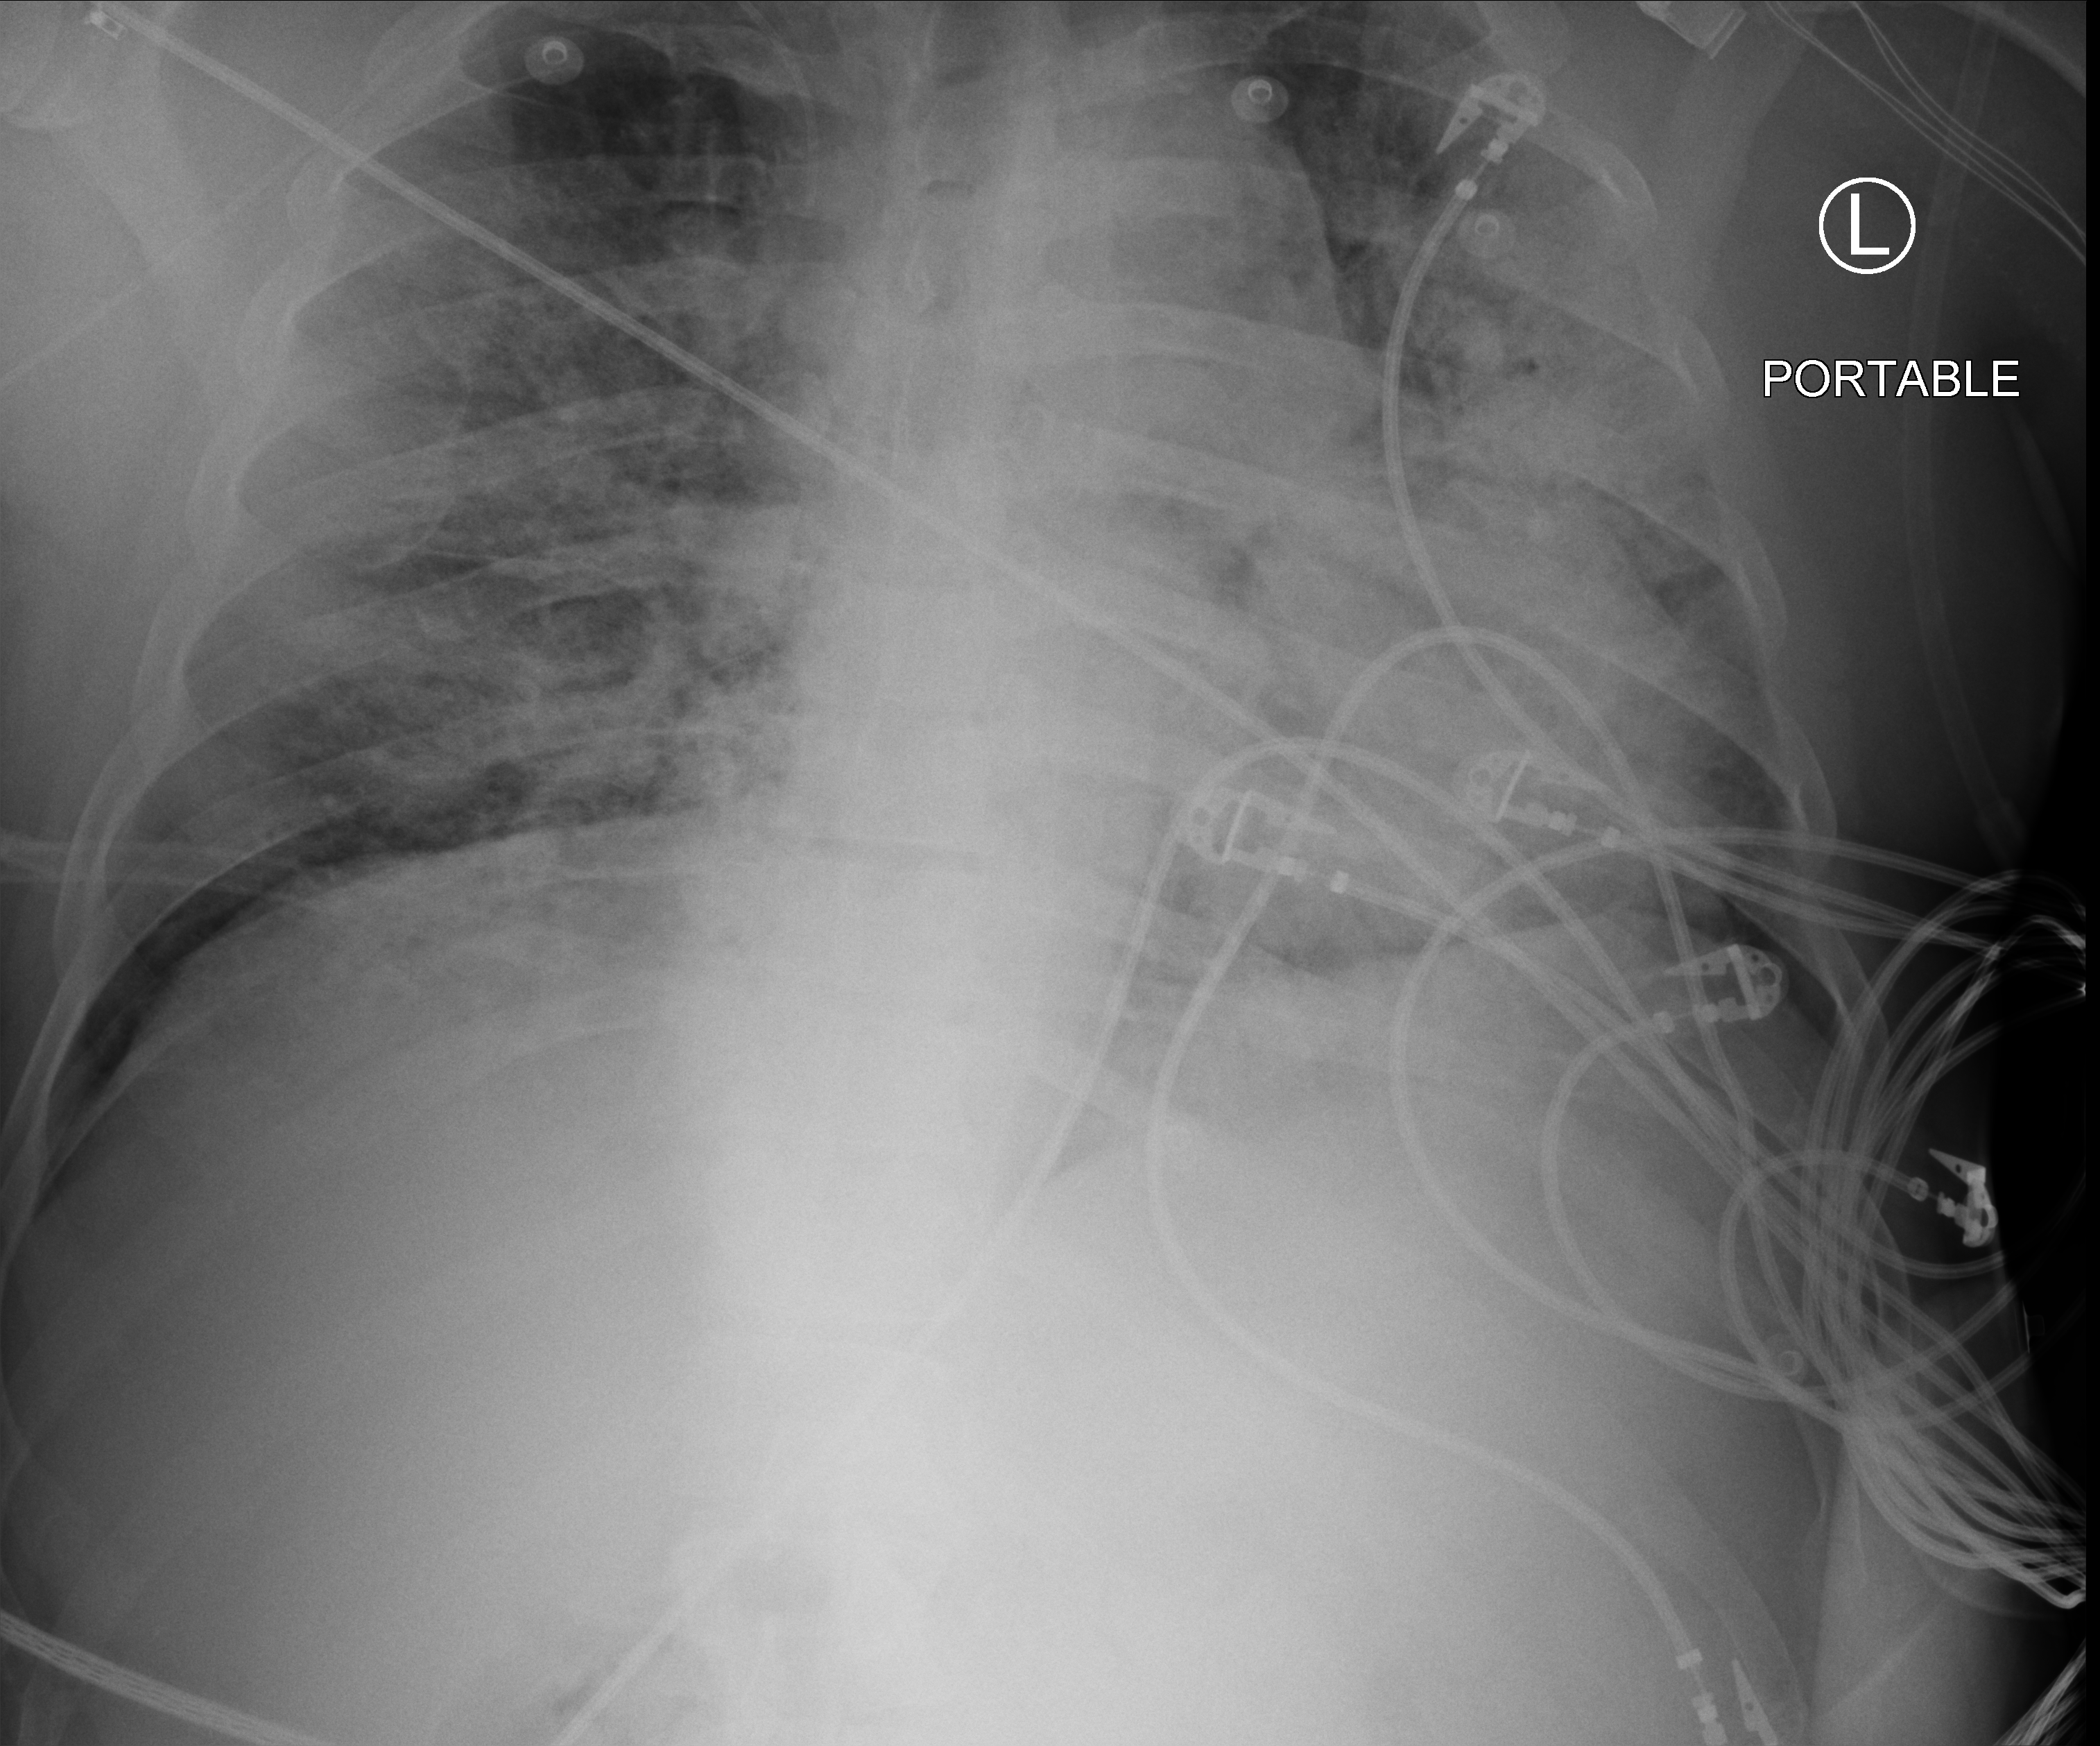
Bedside chest radiograph (computed radiography), anteroposterior (AP) projection. Patient hospitalised with COVID-19; male, aged 18–59 years.
Admission-level facts for this patient (not findings on this image; timing relative to this image not recorded): length of hospital stay: 52 days; other chronic lung disease (admission record): no.